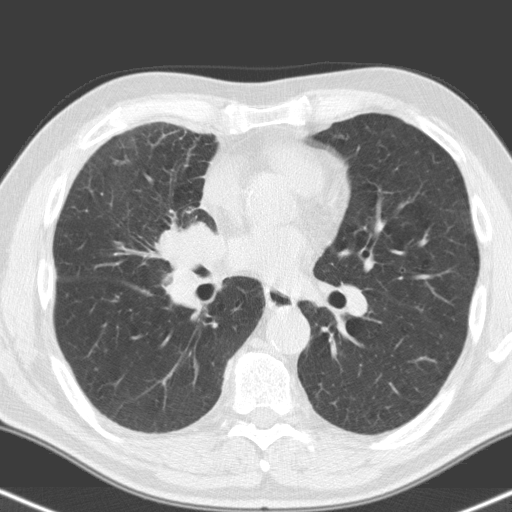
Low-dose screening chest CT, one axial slice. Position 82 of 160 along the scan axis. 120 kVp. Lung window (W 1500 / L -600 HU). 512 × 512 image matrix, field of view 324 × 324 mm.
Structures marked on this image (outlined manually by an expert reader):
- lesion 1 (tumor, hilum of right lung): bounding box <159,221,223,307> (left, top, right, bottom; pixels)